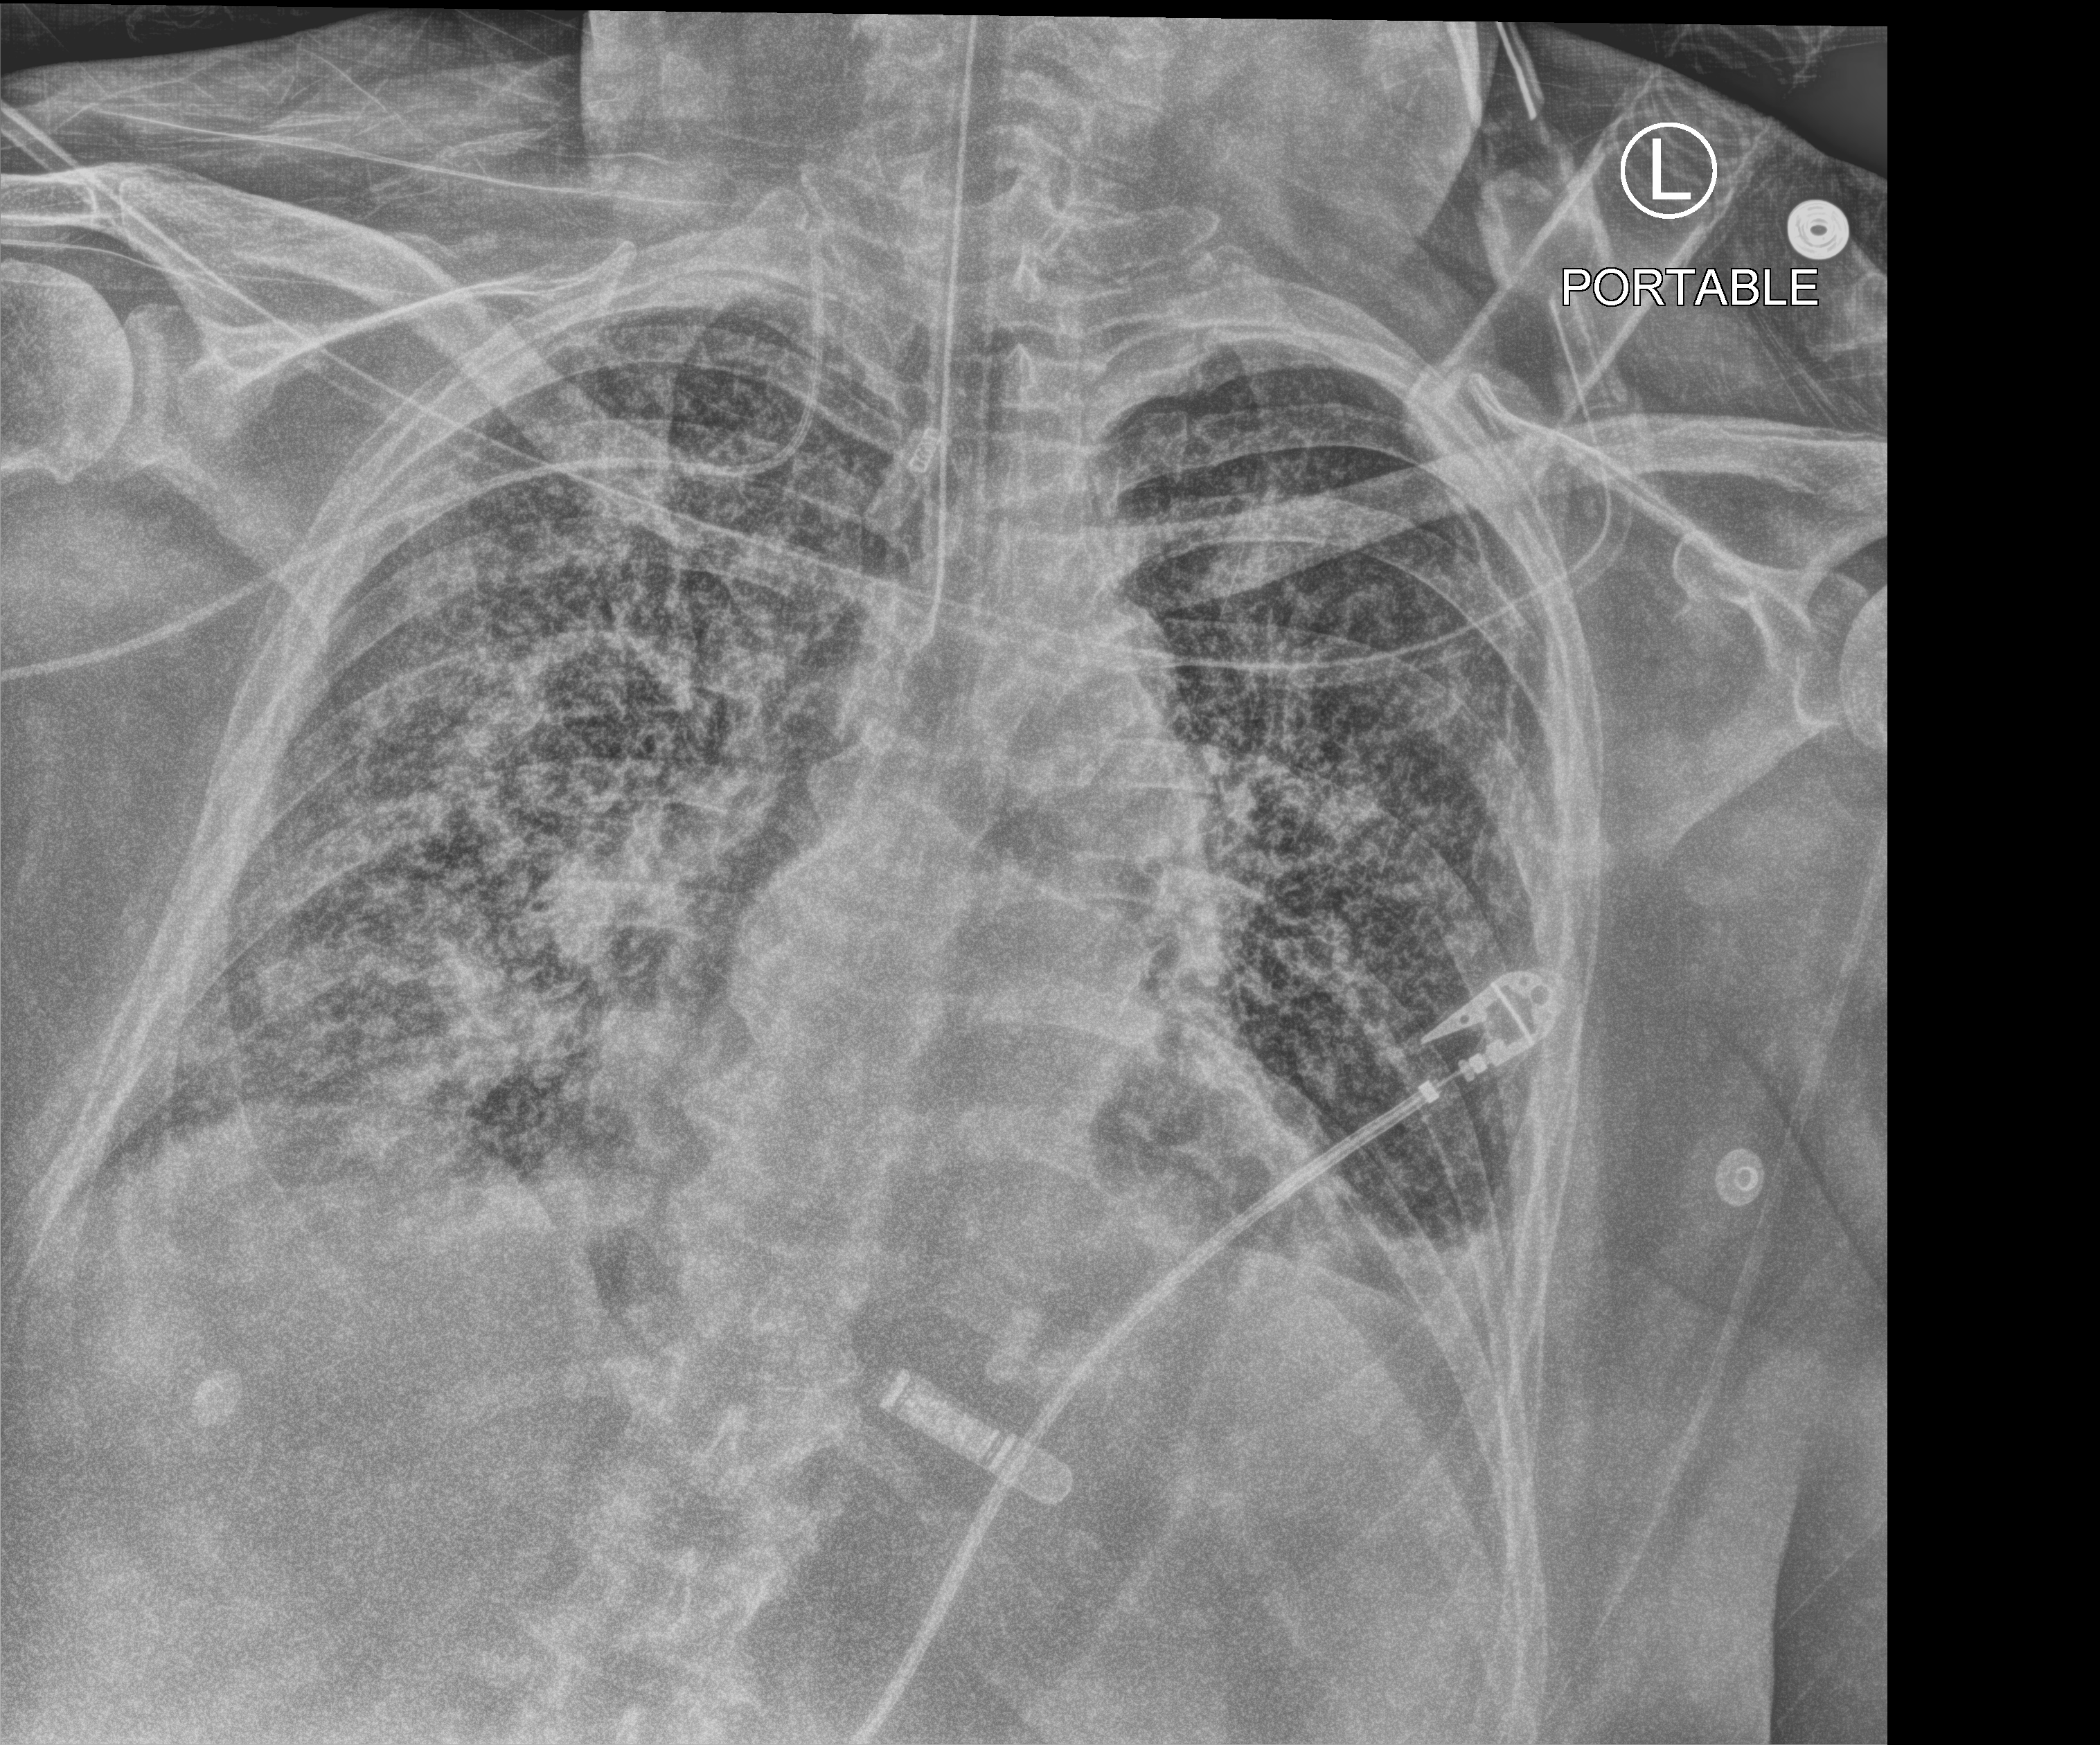
Portable chest radiograph; anteroposterior (AP) projection. Patient hospitalised with COVID-19; female, aged 60–74 years.
Admission-level facts for this patient (not findings on this image; timing relative to this image not recorded): length of hospital stay: 28 days; COPD (admission record): no; admitted to intensive care during this hospital stay: yes.